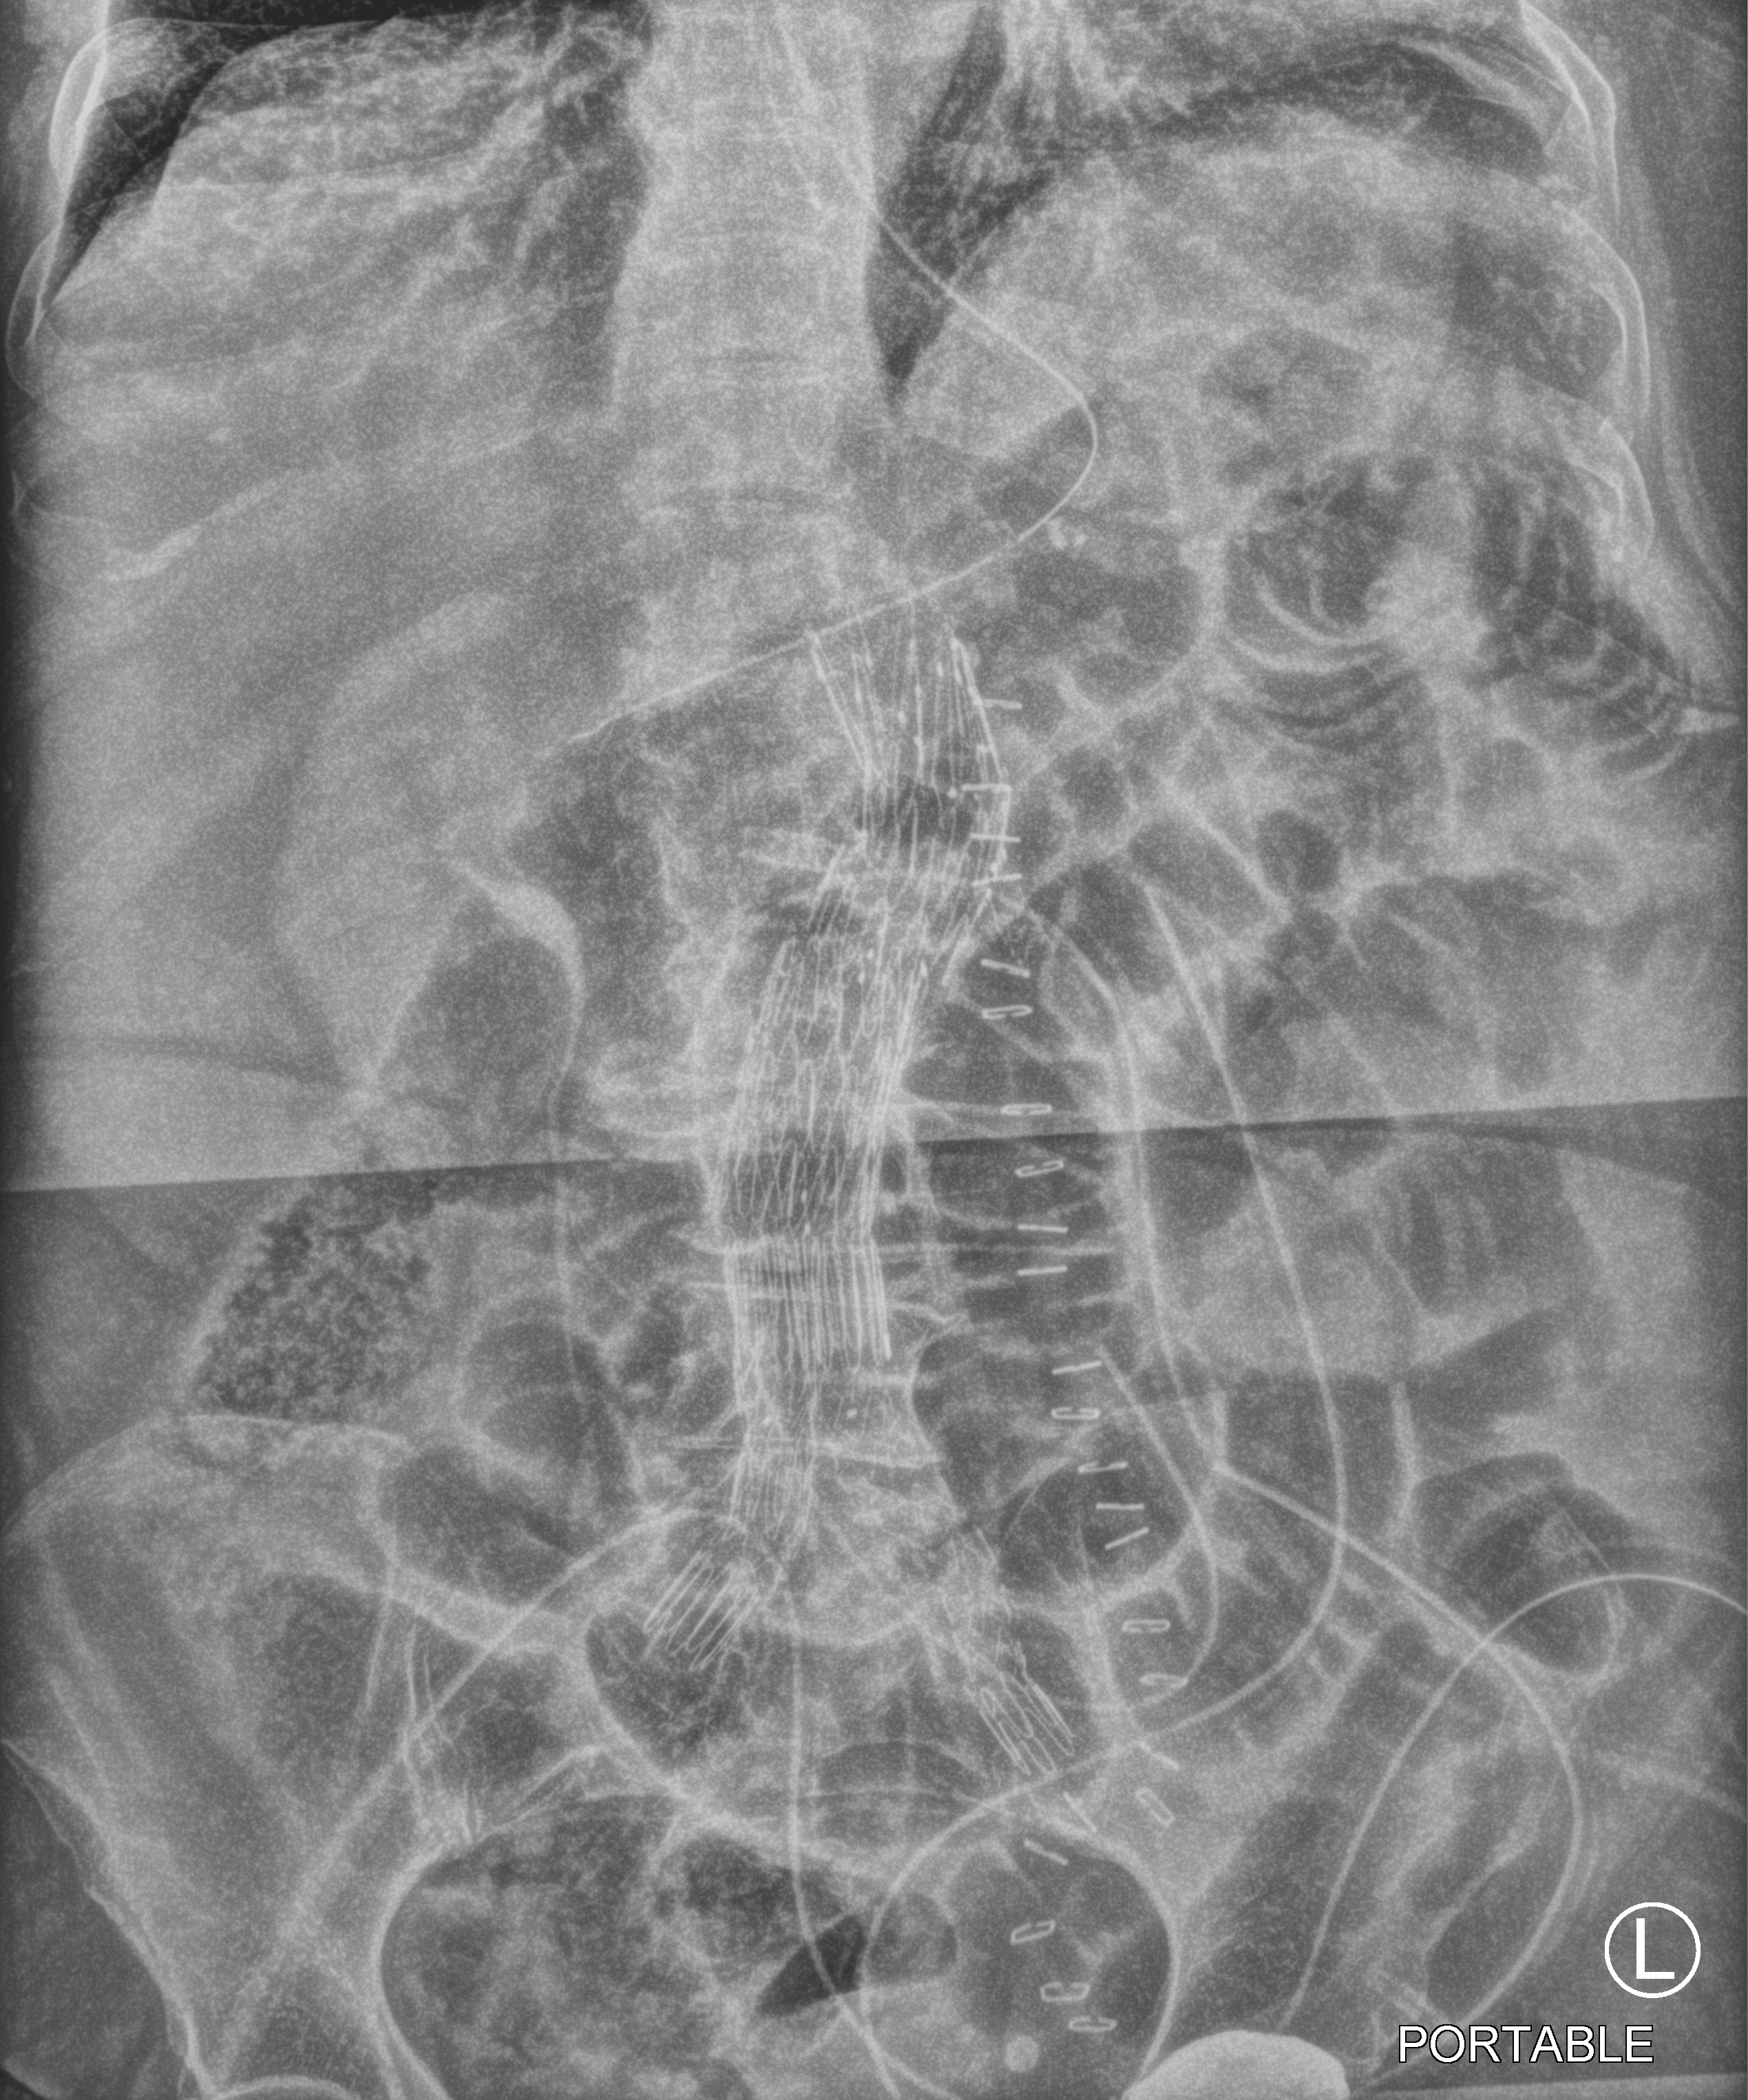
Bedside abdomen radiograph (computed radiography); anteroposterior (AP) projection. Patient hospitalised with COVID-19; female, aged 60–74 years.
Admission-level facts for this patient (not findings on this image; timing relative to this image not recorded): length of hospital stay: 9 days; admitted to intensive care during this hospital stay: yes.